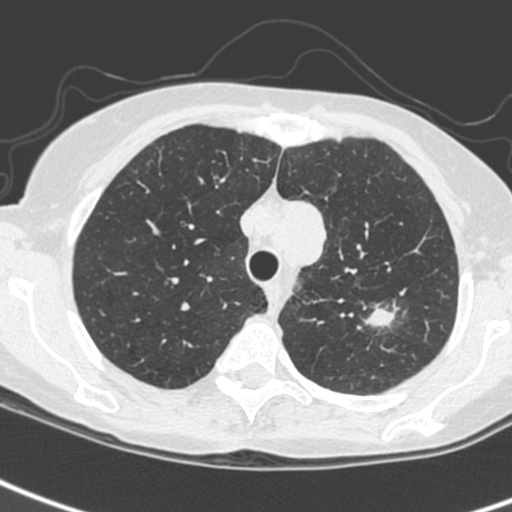
Low-dose screening chest CT, one axial slice. Slice 195 of 242 in the series (ordered by position). 120 kVp. Lung window (W 1500 / L -600 HU). 1.3 mm slice thickness. 512 × 512 image matrix, field of view 284 × 284 mm.
Annotated regions visible in this slice (expert manual segmentation):
- lesion 1 (tumor, upper lobe of left lung): bounding box <368,308,396,327> (left, top, right, bottom; pixels)
- lesion 3 (tumor, upper lobe of left lung): <293,200,327,266>